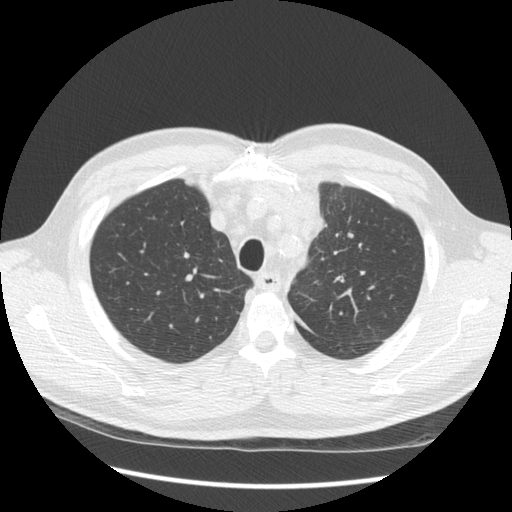
Low-dose screening chest CT, one axial slice. Reconstruction kernel STANDARD. Lung window (W 1500 / L -600 HU). 2.5 mm slice thickness. 512 × 512 image matrix.
Annotated regions visible in this slice (expert manual segmentation):
- lesion 1 (tumor, upper lobe of left lung): bounding box <295,186,324,241> (left, top, right, bottom; pixels)